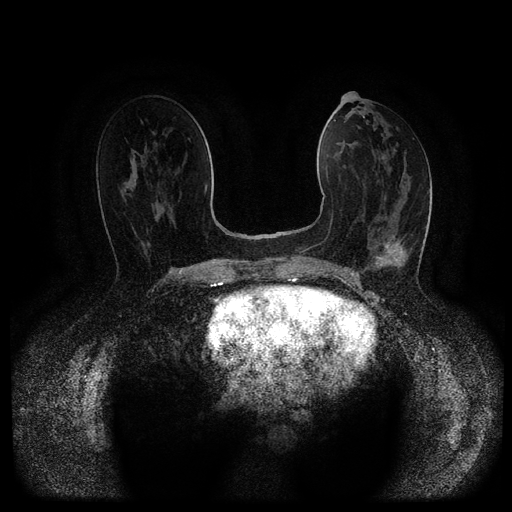
Breast MRI (dynamic contrast-enhanced, multi-phase), one axial slice. Slice 51 of 116 in the series (ordered by position). Dynamic contrast-enhanced series, time point 2 of 5 at this slice position (early post-contrast). 1.5 T. TE 2.6 ms, TR 5.4 ms. 2 mm slice thickness. 512 × 512 image matrix. Patient: female, 61 years.
Structures marked on this image (semi-automatically segmented with operator editing):
- breast lesion (labelled 'tumour' in the annotation; benign lesions carry a separate 'benign' label): bounding box <373,235,395,269> (left, top, right, bottom; pixels)